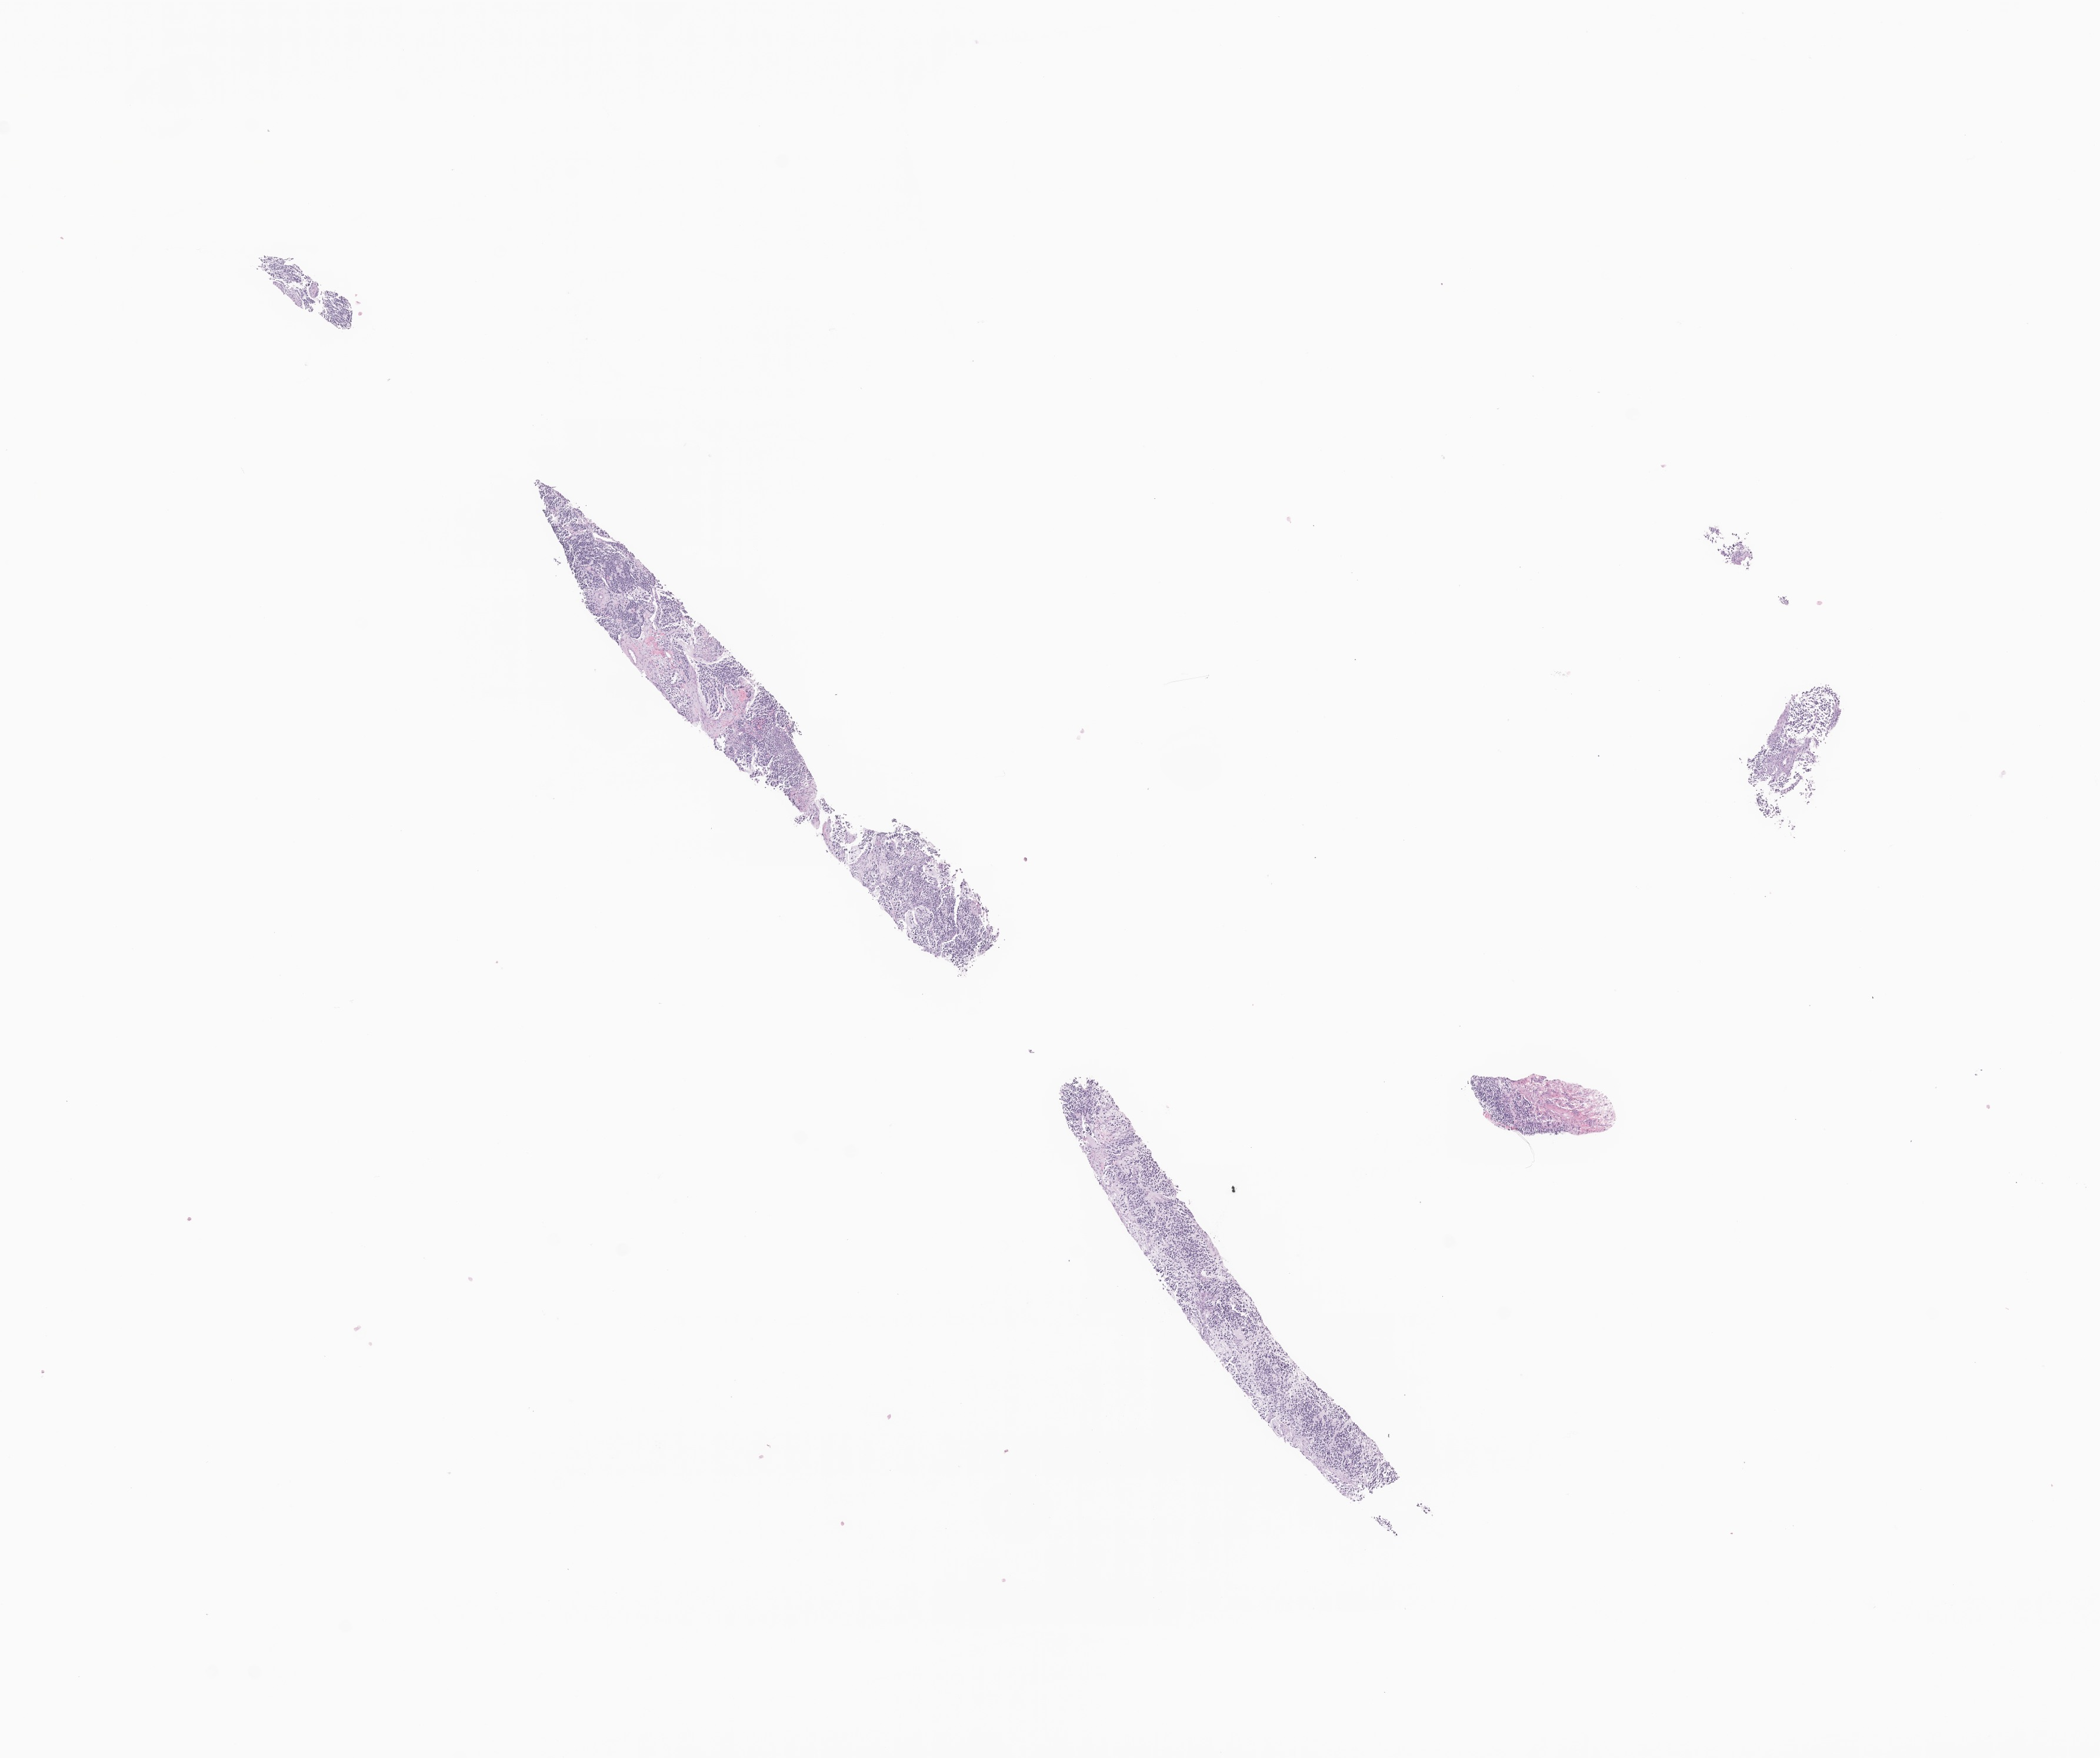
Digitized hematoxylin and eosin (H&E)-stained section of tumor tissue from the retroperitoneum, a low-resolution overview of the entire scanned area, about 15.1 x 12.6 mm. Patient female; age 319 days.
Specimen: FFPE section.